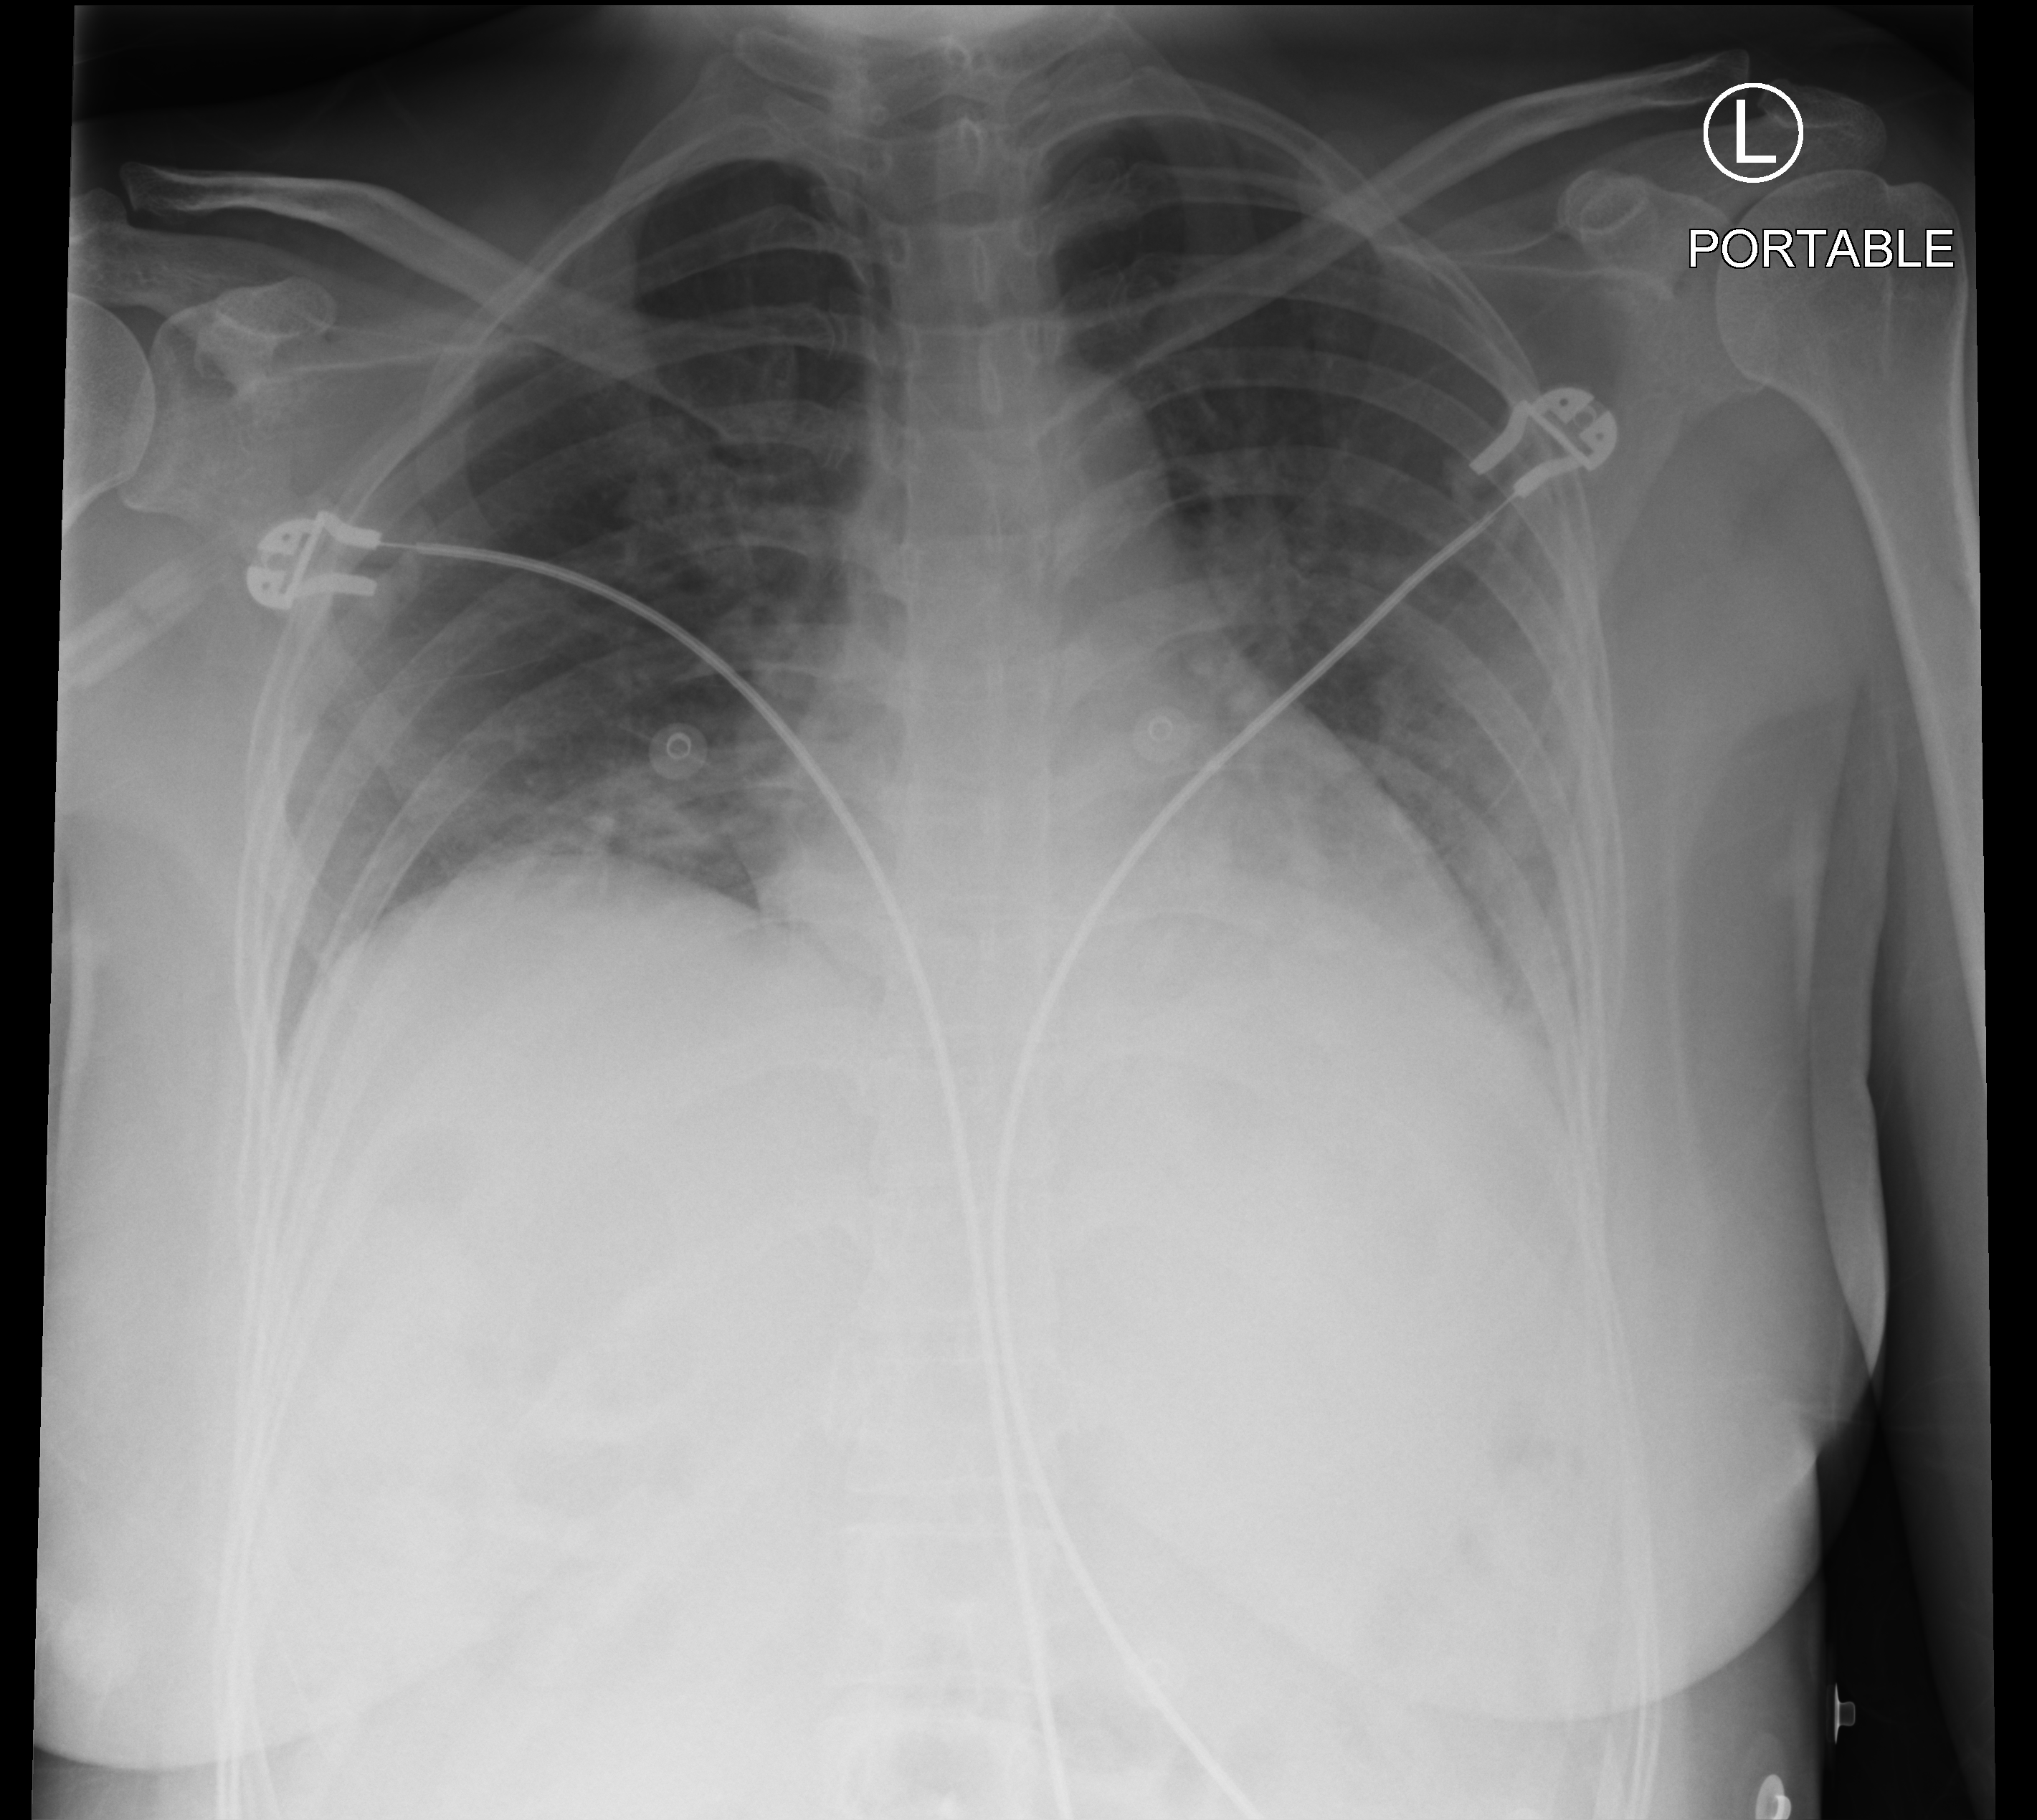
Portable chest radiograph; anteroposterior (AP) projection. Female patient hospitalised with COVID-19, age 18–59 years.
From the hospital-stay record, not from the radiograph (when in the stay this image was taken is not recorded): admitted to intensive care during this hospital stay: no; mechanically ventilated during this hospital stay: no.